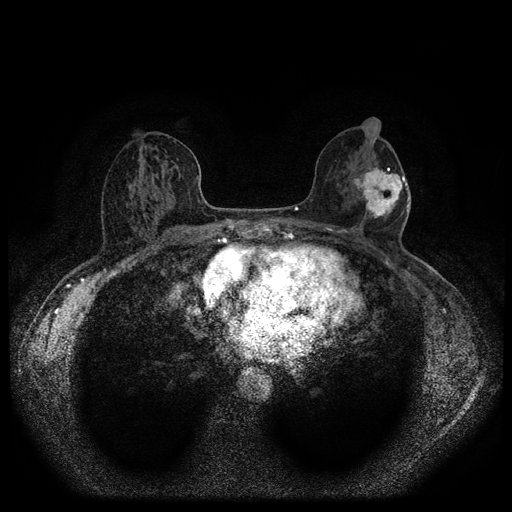
Breast MRI (dynamic contrast-enhanced, multi-phase), one axial slice. Slice 52 of 116 in the series (ordered by position). Dynamic contrast-enhanced series, time point 2 of 5 at this slice position (early post-contrast). 1.5 T. TE 2.7 ms, TR 5.4 ms. 512 × 512 image matrix, field of view 330 × 330 mm. Patient: female, 56 years.
Annotated regions visible in this slice (semi-automatic segmentation, software-assisted and operator-edited):
- breast lesion (labelled 'tumour' in the annotation; benign lesions carry a separate 'benign' label): bounding box <353,167,404,221> (left, top, right, bottom; pixels)